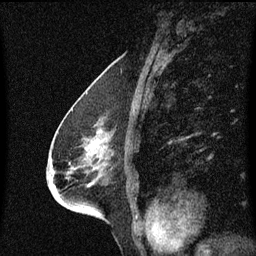
Breast MRI (dynamic contrast-enhanced), one sagittal slice; dynamic contrast-enhanced series, image 2 of 3 at this slice position (ordered by acquisition); 1.5 T; TE 4.2 ms, TR 8.4 ms; 2 mm slice thickness; 256 × 256 image matrix, field of view 200 × 200 mm. Female patient, age 68 years. From the clinical record (not read from this slice): setting: breast cancer imaged before/during neoadjuvant chemotherapy; receptor status: triple-negative.
Outlined on this slice (semi-automatic segmentation, software-assisted and operator-edited):
- analysis volume of interest (the breast-tissue region the enhancement analysis was run in; not a lesion): box from (x=44, y=114) to (x=132, y=203) px
- tumour enhancement mask (voxels above the 70 % enhancement threshold inside the analysis volume of interest): (x=88, y=132)–(x=104, y=157)